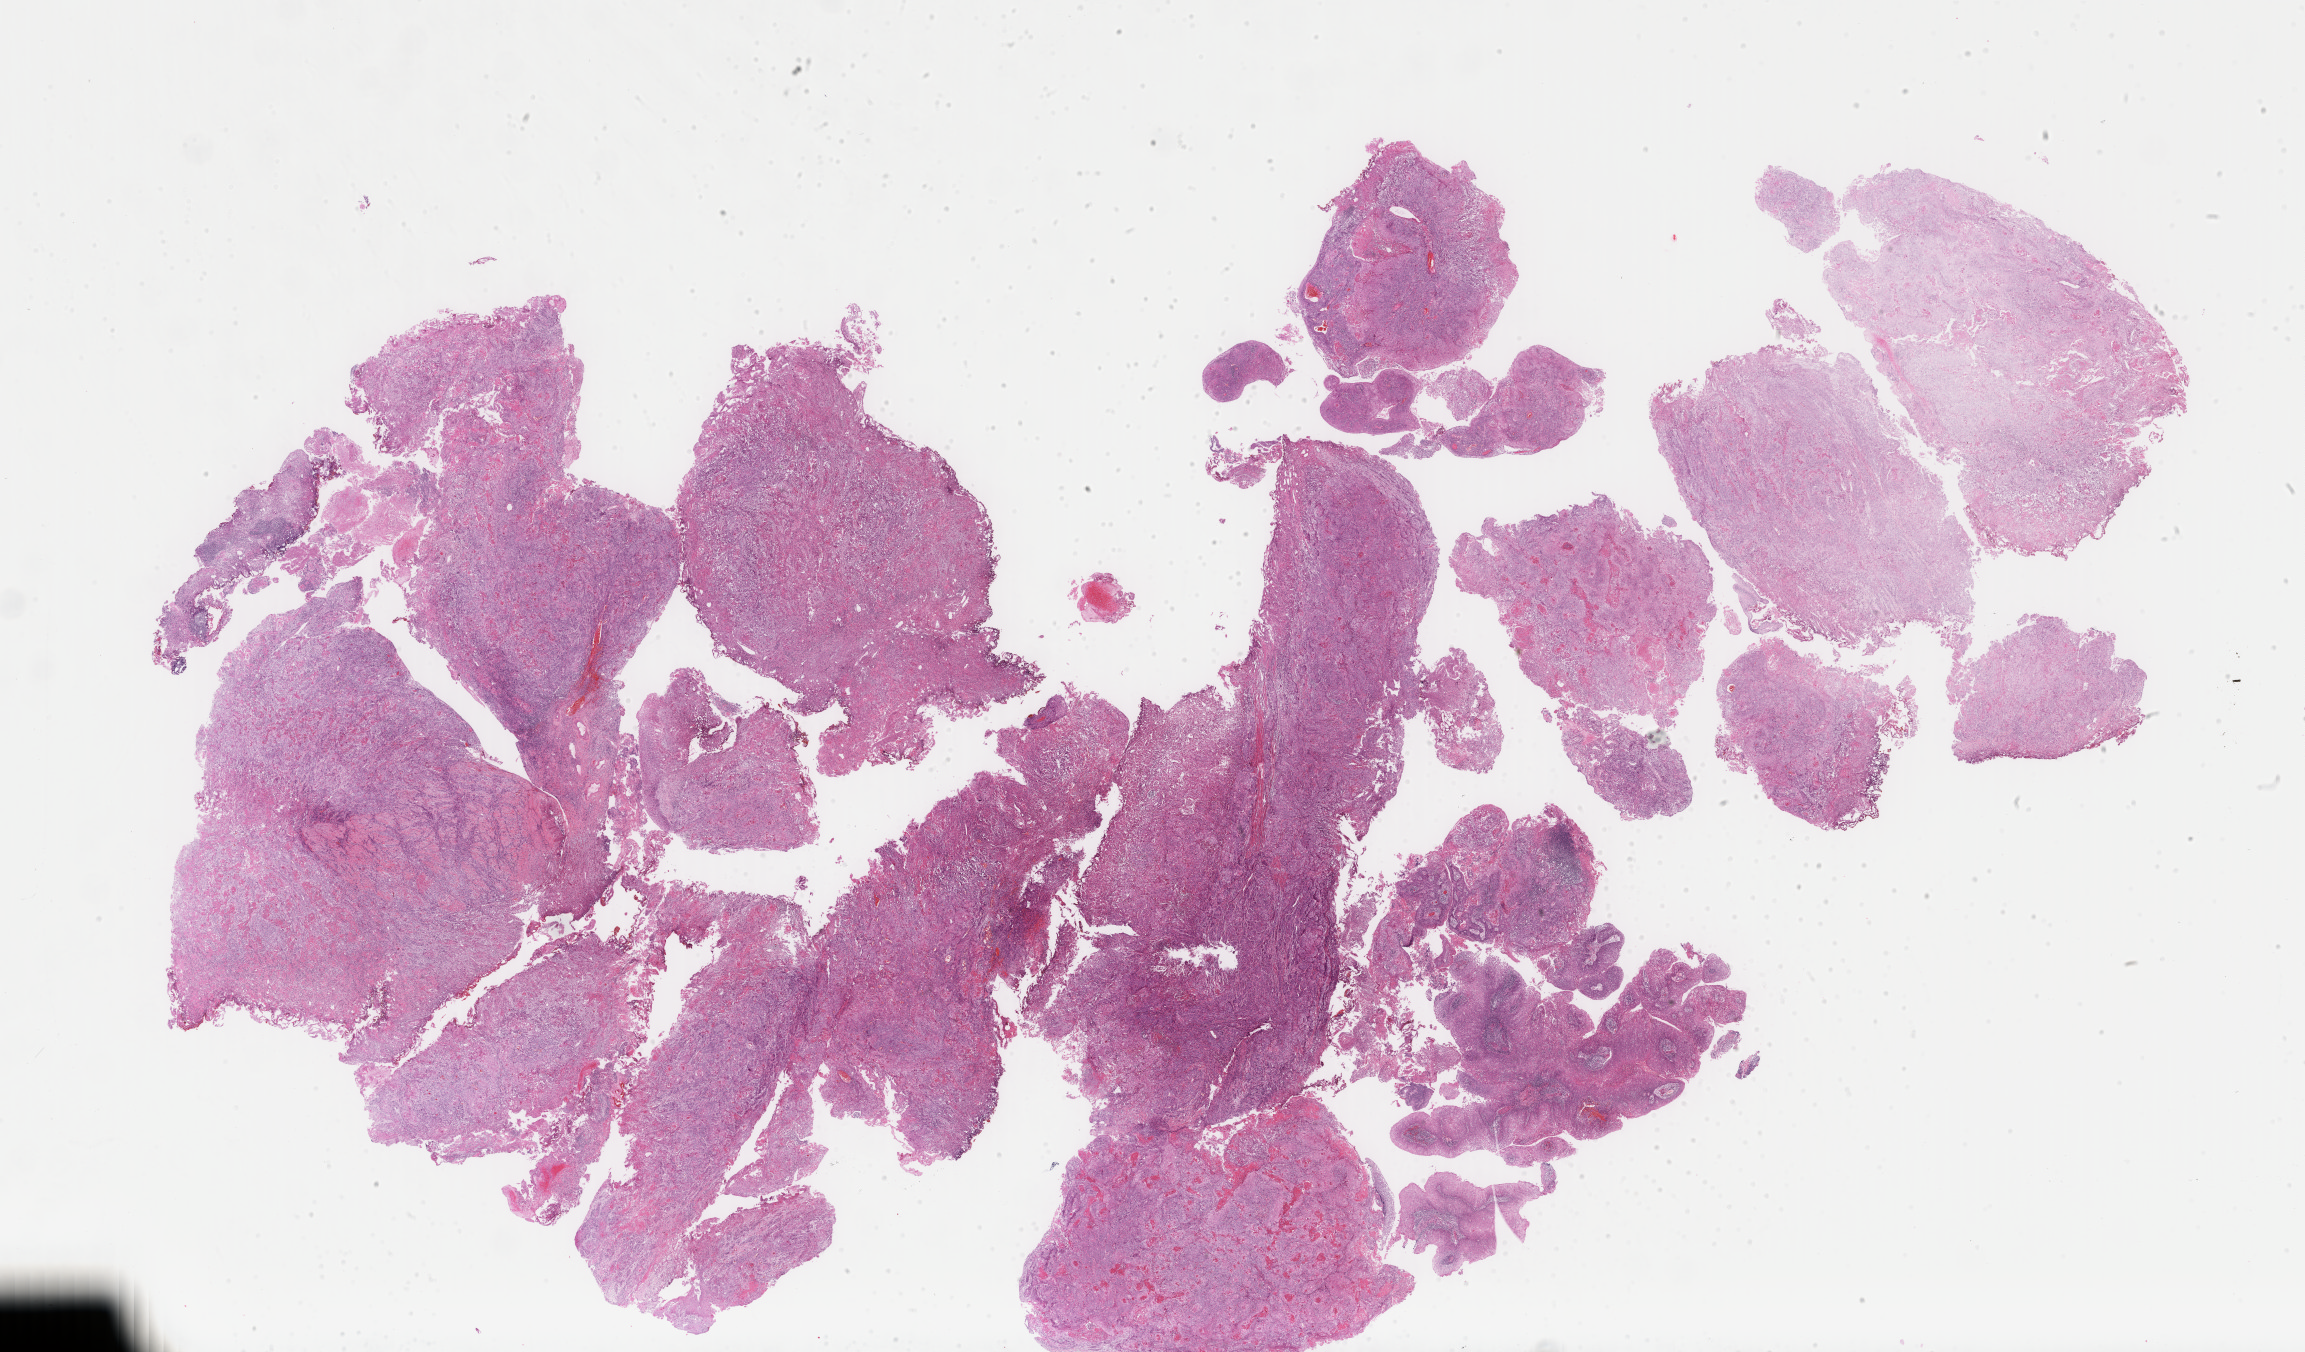
Whole-slide histology image, H&E — whole scanned area (about 36.6 x 21.5 mm, slide scanned at 40x) shown as a low-resolution overview; formalin-fixed paraffin-embedded (FFPE) diagnostic section; bladder, primary tumour sample. Female patient; age at initial diagnosis 56 years. Histologic grade: high grade.
Histologic diagnosis: Transitional cell carcinoma. AJCC pathologic stage: II (6th edition).